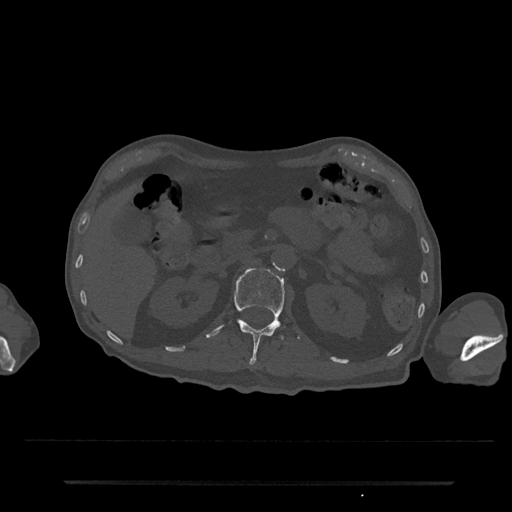
CT including the spine, one axial slice. Slice 126 of 797 in the series (ordered by position). Reconstruction kernel Br40s/3. 120 kVp. Bone window (W 1800 / L 400 HU). 0.5 mm slice thickness. 512 × 512 image matrix. Patient: male, 74 years. Case-level facts recorded for this patient, not image findings: primary cancer: prostate.
Structures marked on this image (semi-automatically segmented with operator editing):
- L1 vertebra: bounding box [x1, y1, x2, y2] px = [205, 268, 300, 364]